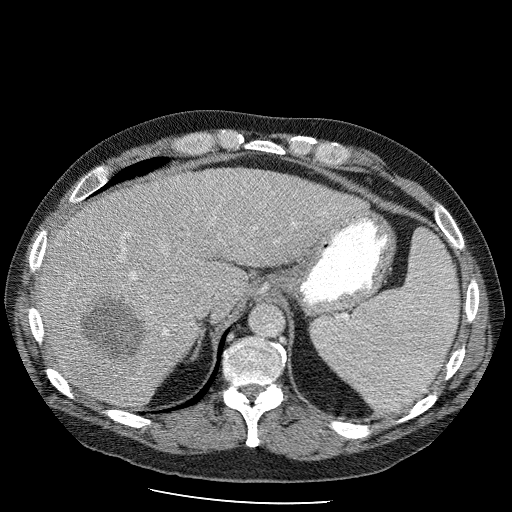
Contrast-enhanced abdominal CT (liver protocol), one axial slice. Slice 76 of 98 in the series (ordered by position). 120 kVp. Soft-tissue window (W 400 / L 40 HU). 2.5 mm slice thickness. 512 × 512 image matrix, field of view 400 × 400 mm. Case-level facts recorded for this patient, not image findings: diagnosis: hepatocellular carcinoma (patient treated with transarterial chemoembolisation; whether this scan precedes or follows treatment is not stated here); TNM stage (as recorded): Stage-II; Child-Pugh class: B; tumour differentiation: moderately differentiated; tumour nodularity: uninodular.
Annotated regions visible in this slice (semi-automatically segmented with operator editing):
- liver parenchyma outside the tumour (the mass and vessels are separate outlines, so this box may not span the whole liver): box from (x=36, y=168) to (x=365, y=408) px
- mass: (x=76, y=291)–(x=155, y=362)
- liver vessels: (x=121, y=235)–(x=135, y=277)